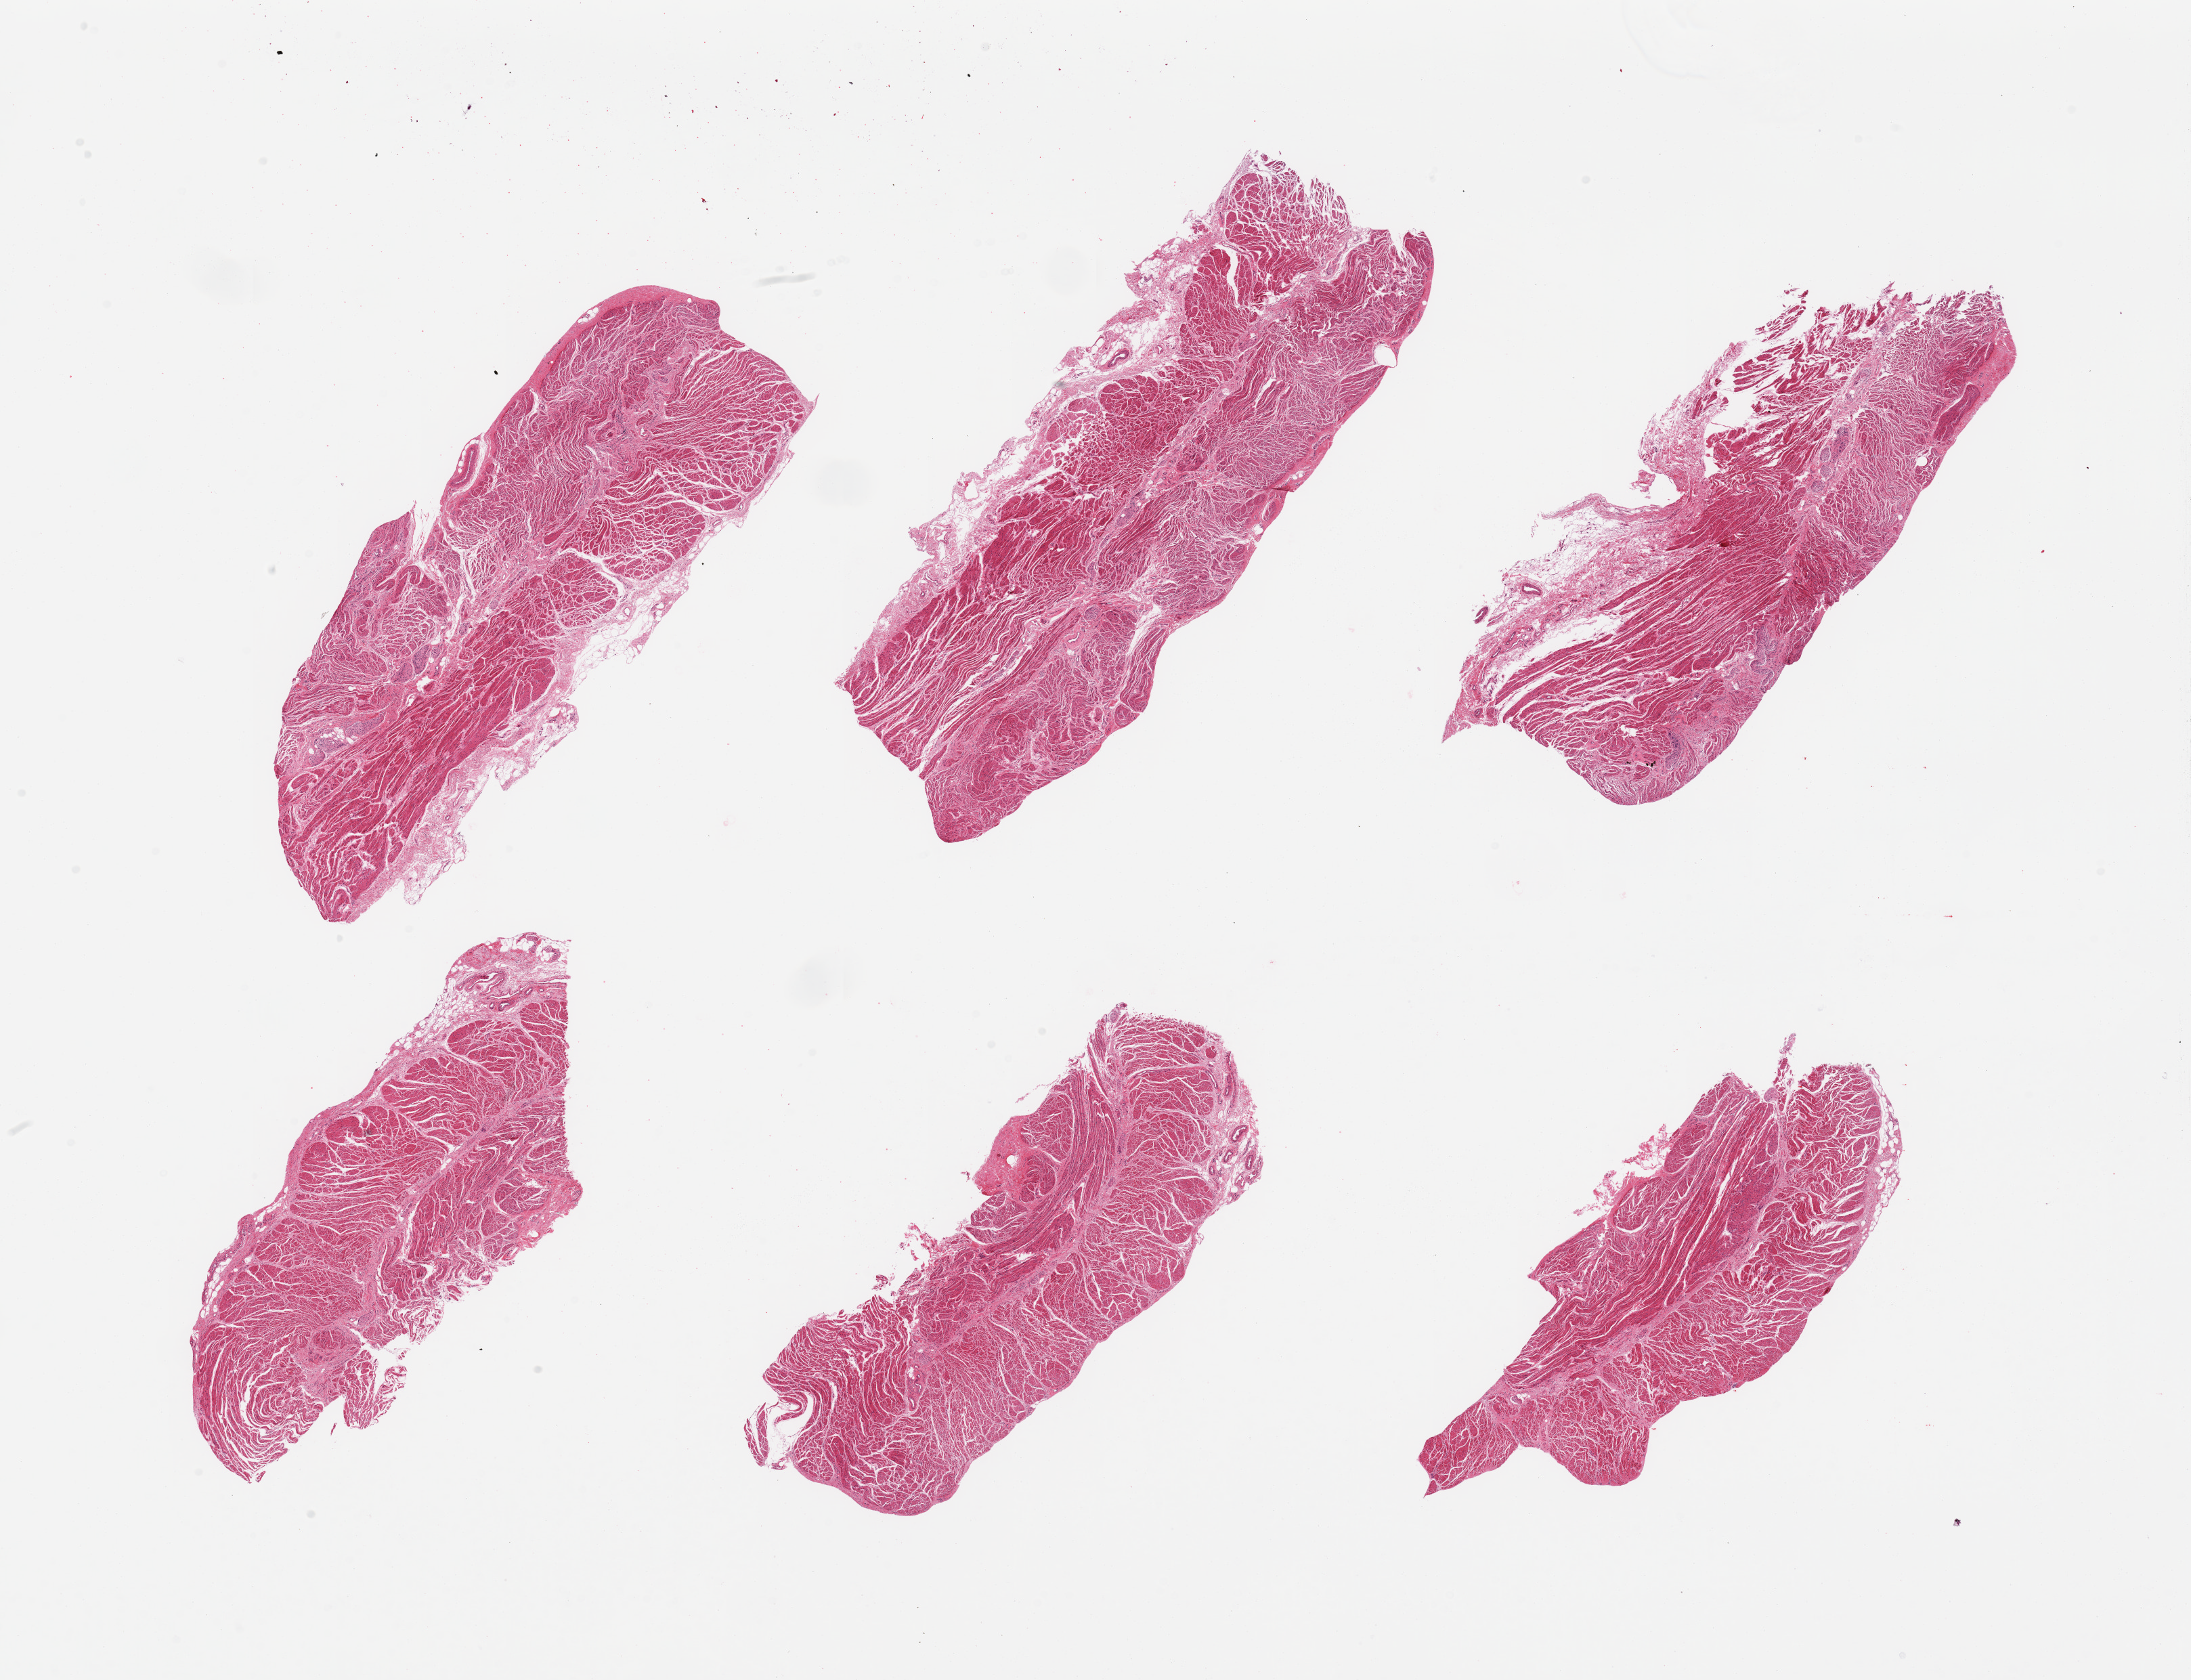
Digitized haematoxylin and eosin-stained section, whole scanned area (about 25.6 x 19.6 mm) shown as a low-resolution overview, PAXgene-fixed paraffin-embedded (PFPE) section, section of gastroesophageal junction (target tissue), tissue donor sample. Donor sex: male.
Reviewer comment on this tissue sample: 6 pieces; target muscularis, some include small component of residual fat.